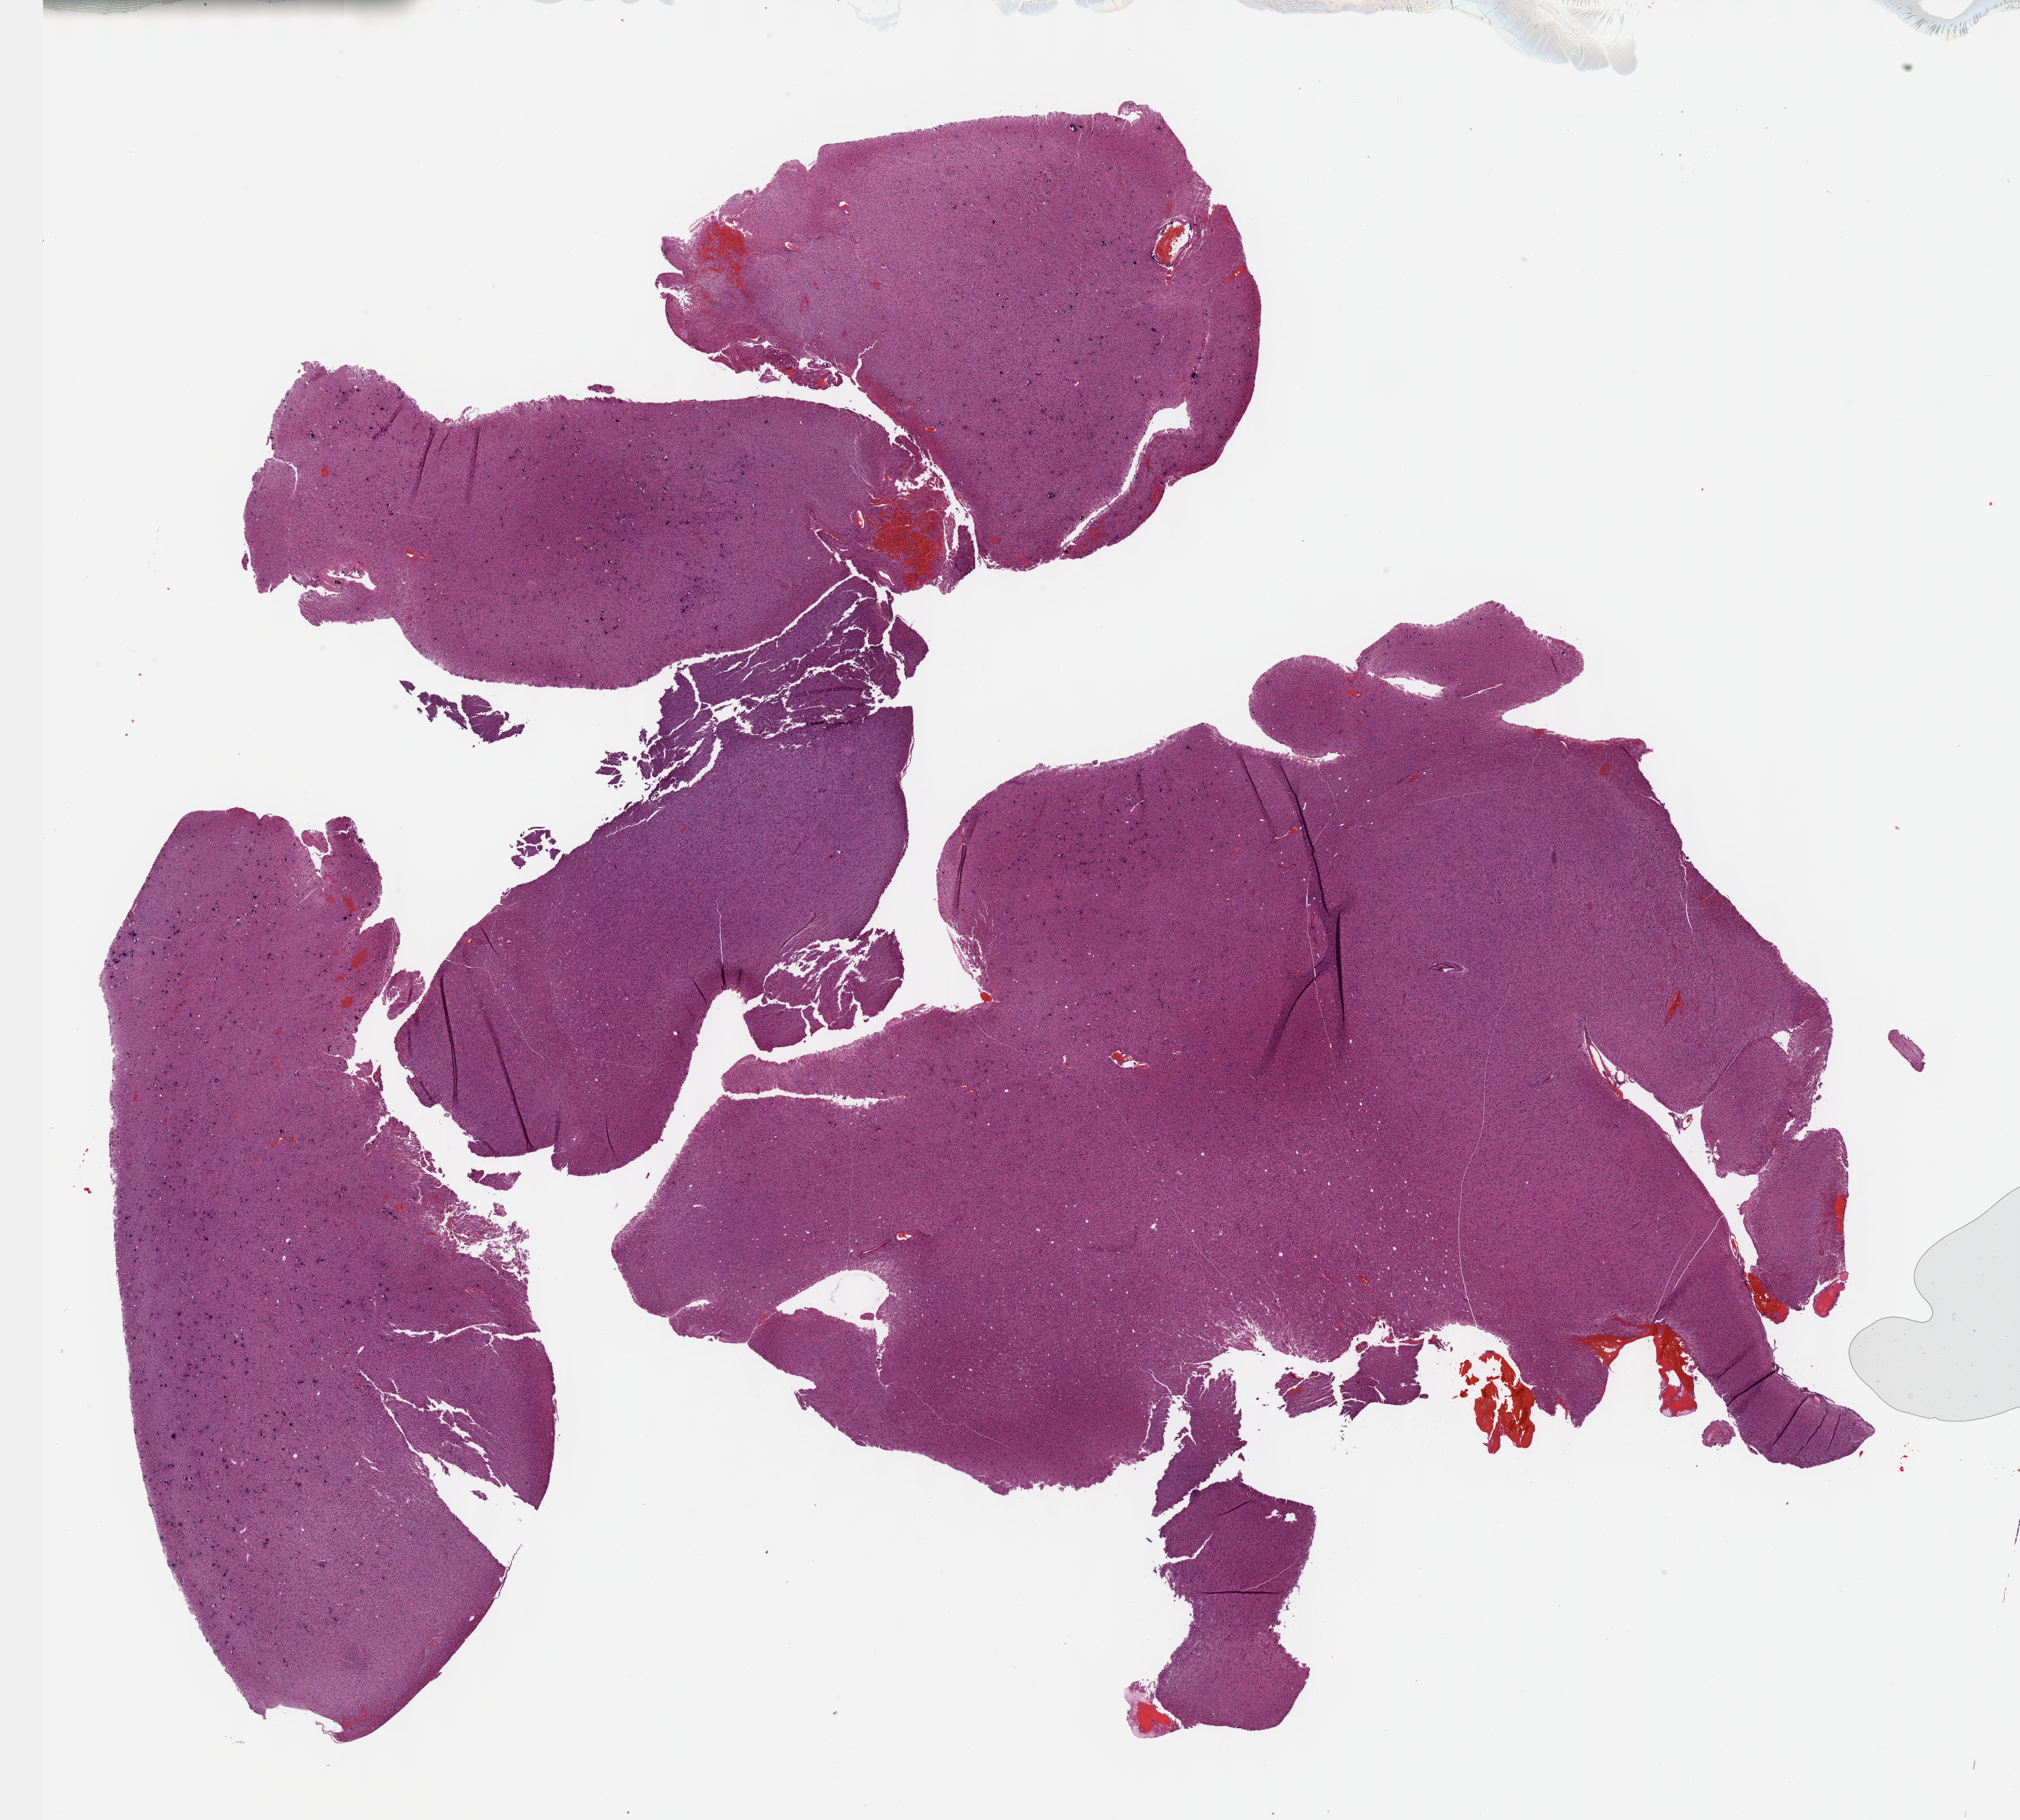
Whole-slide histology image, H&E — shown as a low-resolution overview of the whole scanned area (about 23.6 x 21.3 mm), formalin-fixed paraffin-embedded (FFPE) diagnostic section, brain, primary tumour sample. Female patient; age at initial diagnosis 60 years. Histologic grade: G3 (poorly differentiated).
Pathologic diagnosis: Astrocytoma, anaplastic (cerebrum).